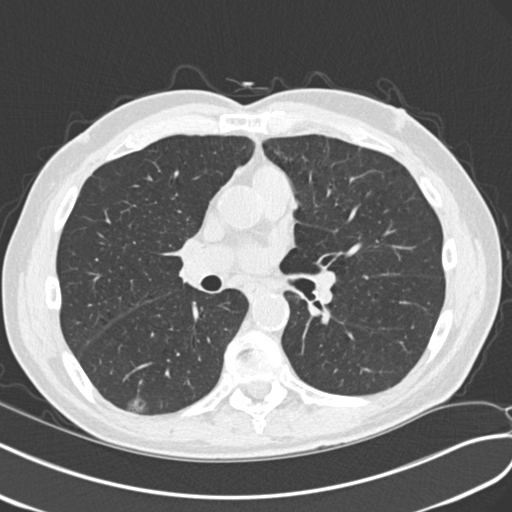
Low-dose screening chest CT, axial slice, second annual screen, lung window (W 1500 / L -600 HU), standard (soft-tissue) reconstruction kernel (B30f). Male, age 68 years at enrolment. Current smoker at enrolment.
Expert-annotated lung lesion, bounding box [x1, y1, x2, y2] px = [108, 383, 158, 421]. The screening reader recorded 4 non-calcified nodules or masses ≥4 mm on this exam (right upper lobe, left upper lobe, right upper lobe, right lower lobe); which of them this box marks is not recorded. Lung cancer was diagnosed 653 days after this screen (after the third annual screen): non-small cell carcinoma, right lower lobe, poorly differentiated (G3), stage IA (AJCC 6th edition), 23 mm at pathology.